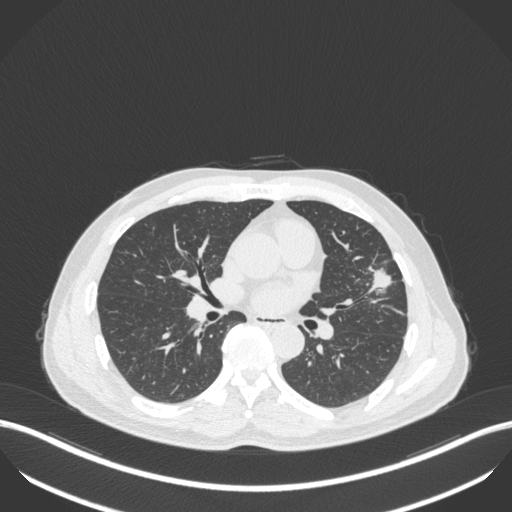
Chest CT, one axial slice. Slice 207 of 418 in the series (ordered by position). Lung window (W 1500 / L -600 HU). 512 × 512 image matrix. Male patient, age 55 years. From the clinical record (not read from this slice): clinical TNM (as recorded): T1c N0 M0.
Structures marked on this image (rectangle marked by the reading radiologist):
- lung tumour (recorded histology: adenocarcinoma): bounding box [x1, y1, x2, y2] px = [367, 262, 394, 294]